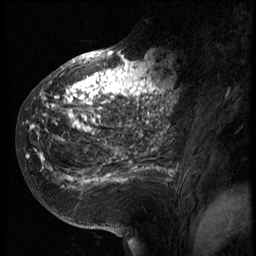
Breast MRI (dynamic contrast-enhanced), one sagittal slice. Slice 32 of 66 in the series (ordered by position). 3 images stored at this slice position (order not interpretable as contrast timing). 1.5 T. TE 4.2 ms, TR 8.9 ms. 256 × 256 image matrix, field of view 200 × 200 mm. Female patient, age 39 years. From the clinical record (not read from this slice): setting: breast cancer imaged before/during neoadjuvant chemotherapy; receptor status: HER2-positive.
Annotated regions visible in this slice (semi-automatic segmentation, software-assisted and operator-edited):
- analysis volume of interest (the breast-tissue region the enhancement analysis was run in; not a lesion): bounding box (x1, y1, x2, y2) in pixels: (29, 44, 166, 196)
- tumour enhancement mask (voxels above the 140 % enhancement threshold inside the analysis volume of interest): (29, 50, 166, 188)